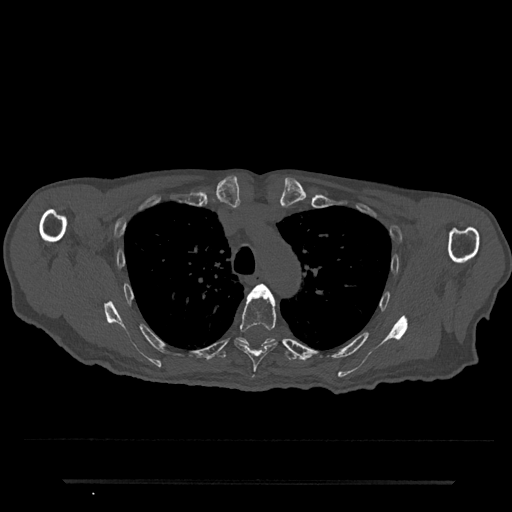
CT including the spine, one axial slice; slice 571 of 797 in the series (ordered by position); reconstruction kernel Br40s/3; 120 kVp; bone window (W 1800 / L 400 HU); 0.5 mm slice thickness; 512 × 512 image matrix. Male patient, age 74 years. From the clinical record (not read from this slice): primary cancer: prostate.
Annotated regions visible in this slice (semi-automatic segmentation, software-assisted and operator-edited):
- T4 vertebra: bounding box [x1, y1, x2, y2] px = [254, 284, 267, 291]
- T5 vertebra: [234, 288, 277, 379]
- T6 vertebra: [215, 337, 298, 361]